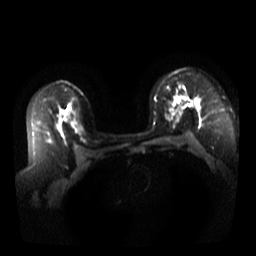
Breast MRI, one axial slice; slice 24 of 44 in the series (ordered by position); diffusion-weighted series; image 2 of 4 stored at this slice position (different b-values; order by instance number); 3 T; 5 mm slice thickness; 256 × 256 image matrix, field of view 340 × 340 mm. Female patient.
Annotated regions visible in this slice (expert manual segmentation):
- tumour on diffusion-weighted imaging: bounding box <177,98,180,103> (left, top, right, bottom; pixels)